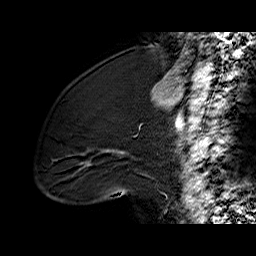
Breast MRI (dynamic contrast-enhanced), one sagittal slice; position 22 of 60 along the scan axis; dynamic contrast-enhanced series, time point 2 of 6 at this slice position (early post-contrast); 1.5 T; TE 6.2 ms, TR 32.4 ms; 4 mm slice thickness; 256 × 256 image matrix. Female patient. Case-level facts recorded for this patient, not image findings: setting: breast cancer imaged before/during neoadjuvant chemotherapy; receptor status: triple-negative.
Structures marked on this image (semi-automatic segmentation, software-assisted and operator-edited):
- analysis volume of interest (the breast-tissue region the enhancement analysis was run in; not a lesion): bounding box (x1, y1, x2, y2) in pixels: (40, 107, 134, 196)
- tumour enhancement mask (voxels above the 100 % enhancement threshold inside the analysis volume of interest): (104, 150, 124, 155)